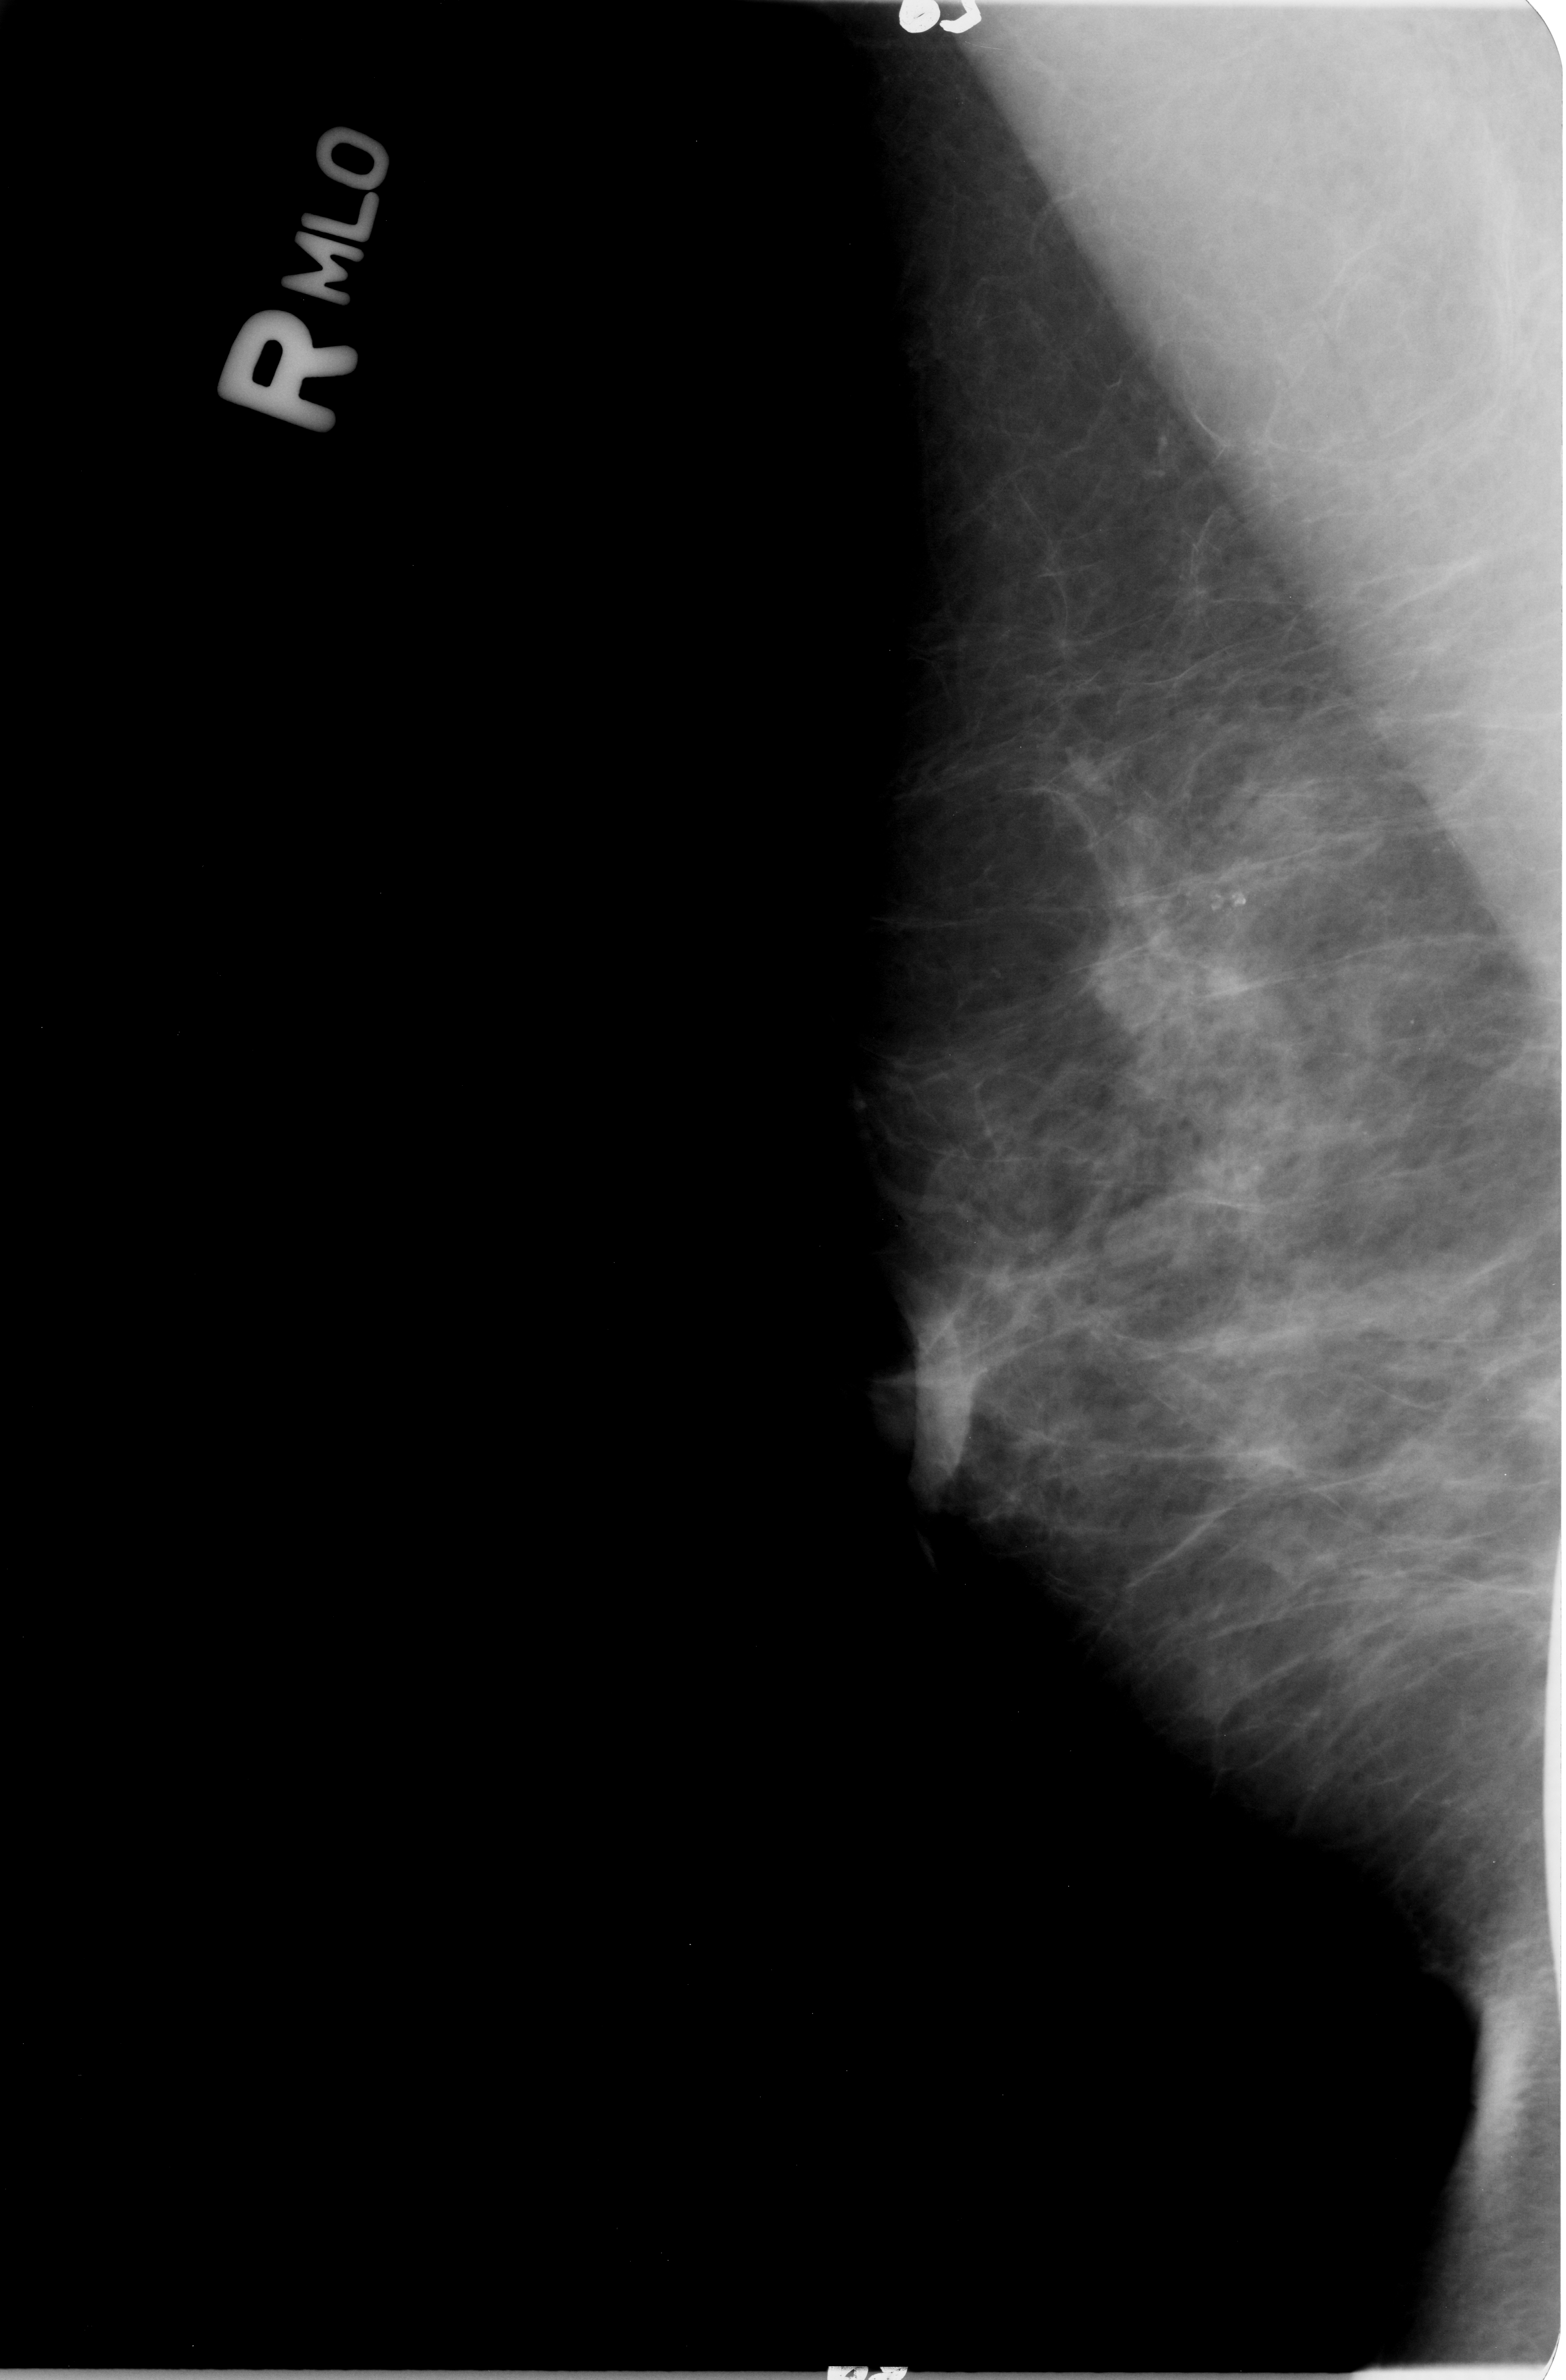
Digitized screen-film mammogram. Right breast. MLO view. Breast composition: heterogeneously dense (BI-RADS density category 3 of 4). 1566 × 2380 image matrix.
Marked abnormalities (boxes around the expert regions of interest):
- Finding 1 of 2: mass, shape architectural distortion; BI-RADS assessment category 2; subtlety rating 3 on a 1 (subtle) to 5 (obvious) scale; pathology (as recorded): benign: bounding box [x1, y1, x2, y2] px = [875, 1371, 920, 1439]
- Finding 2 of 2: mass, shape architectural distortion; BI-RADS assessment category 2; subtlety rating 3 on a 1 (subtle) to 5 (obvious) scale; pathology (as recorded): benign: [899, 1306, 1010, 1478]